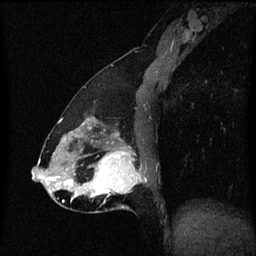
Breast MRI (dynamic contrast-enhanced), one sagittal slice; dynamic contrast-enhanced series, image 2 of 3 at this slice position (ordered by acquisition); 1.5 T; TE 4.2 ms, TR 8.4 ms; 2 mm slice thickness; 256 × 256 image matrix, field of view 200 × 200 mm. Patient: female, 47 years.
Annotated regions visible in this slice (semi-automatic segmentation, software-assisted and operator-edited):
- analysis volume of interest (the breast-tissue region the enhancement analysis was run in; not a lesion): bounding box <81,138,147,213> (left, top, right, bottom; pixels)
- tumour enhancement mask (voxels above the 70 % enhancement threshold inside the analysis volume of interest): <82,142,142,197>